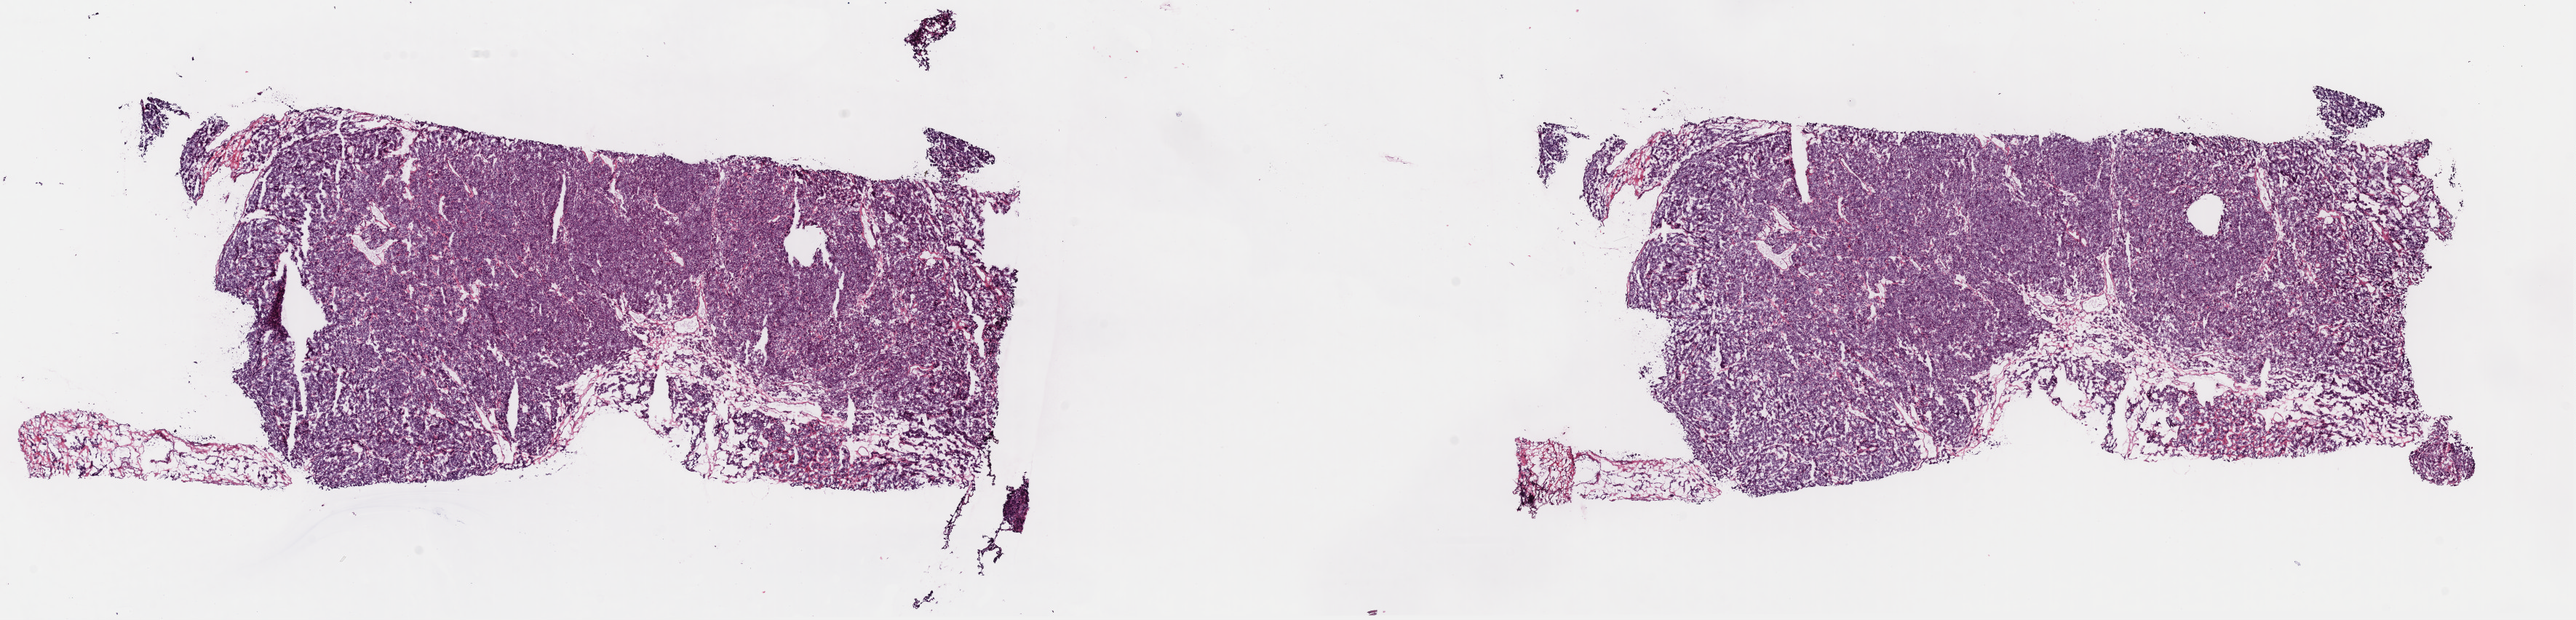
H&E-stained whole-slide image — shown as a low-resolution overview of the whole scanned area (about 28.0 x 6.7 mm); frozen section from the top of the tissue portion; thyroid, primary tumour sample. Male patient; age at initial diagnosis 47 years. Slide review estimates, as recorded: tumour cells 95%, tumour nuclei 95%, normal cells 0%, stromal cells 5%, necrosis 0%. Infiltration values recorded for this section: lymphocyte infiltration 0%, monocyte infiltration 0%, neutrophil infiltration 0%.
• pathologic diagnosis: Papillary carcinoma, follicular variant (thyroid gland)
• AJCC pathologic stage: II
• TNM: T2 N0 M0
• lymph nodes positive (case pathology): 0 of 3 examined